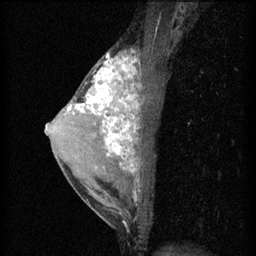
Breast MRI (dynamic contrast-enhanced), one sagittal slice. Slice 34 of 60 in the series (ordered by position). 3 images stored at this slice position (order not interpretable as contrast timing). 1.5 T. TE 4.2 ms, TR 11 ms. 2 mm slice thickness. 256 × 256 image matrix, field of view 180 × 180 mm. Female patient, age 40 years.
Structures marked on this image (semi-automatic segmentation, software-assisted and operator-edited):
- analysis volume of interest (the breast-tissue region the enhancement analysis was run in; not a lesion): bounding box [x1, y1, x2, y2] px = [55, 48, 147, 203]
- tumour enhancement mask (voxels above the 70 % enhancement threshold inside the analysis volume of interest): [69, 50, 140, 199]